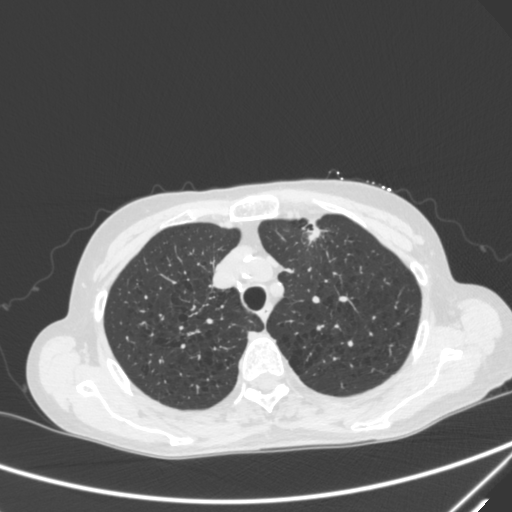
Chest CT, one axial slice; position 236 of 300 along the scan axis; 120 kVp; lung window (W 1500 / L -600 HU); 1 mm slice thickness; 512 × 512 image matrix, field of view 350 × 350 mm. Female patient, age 71 years. Case-level facts recorded for this patient, not image findings: clinical TNM (as recorded): T1c N0 M0; histopathological grade: G2-3.
Outlined on this slice (rectangle marked by the reading radiologist):
- lung tumour (recorded histology: adenocarcinoma): box from (x=293, y=221) to (x=334, y=252) px